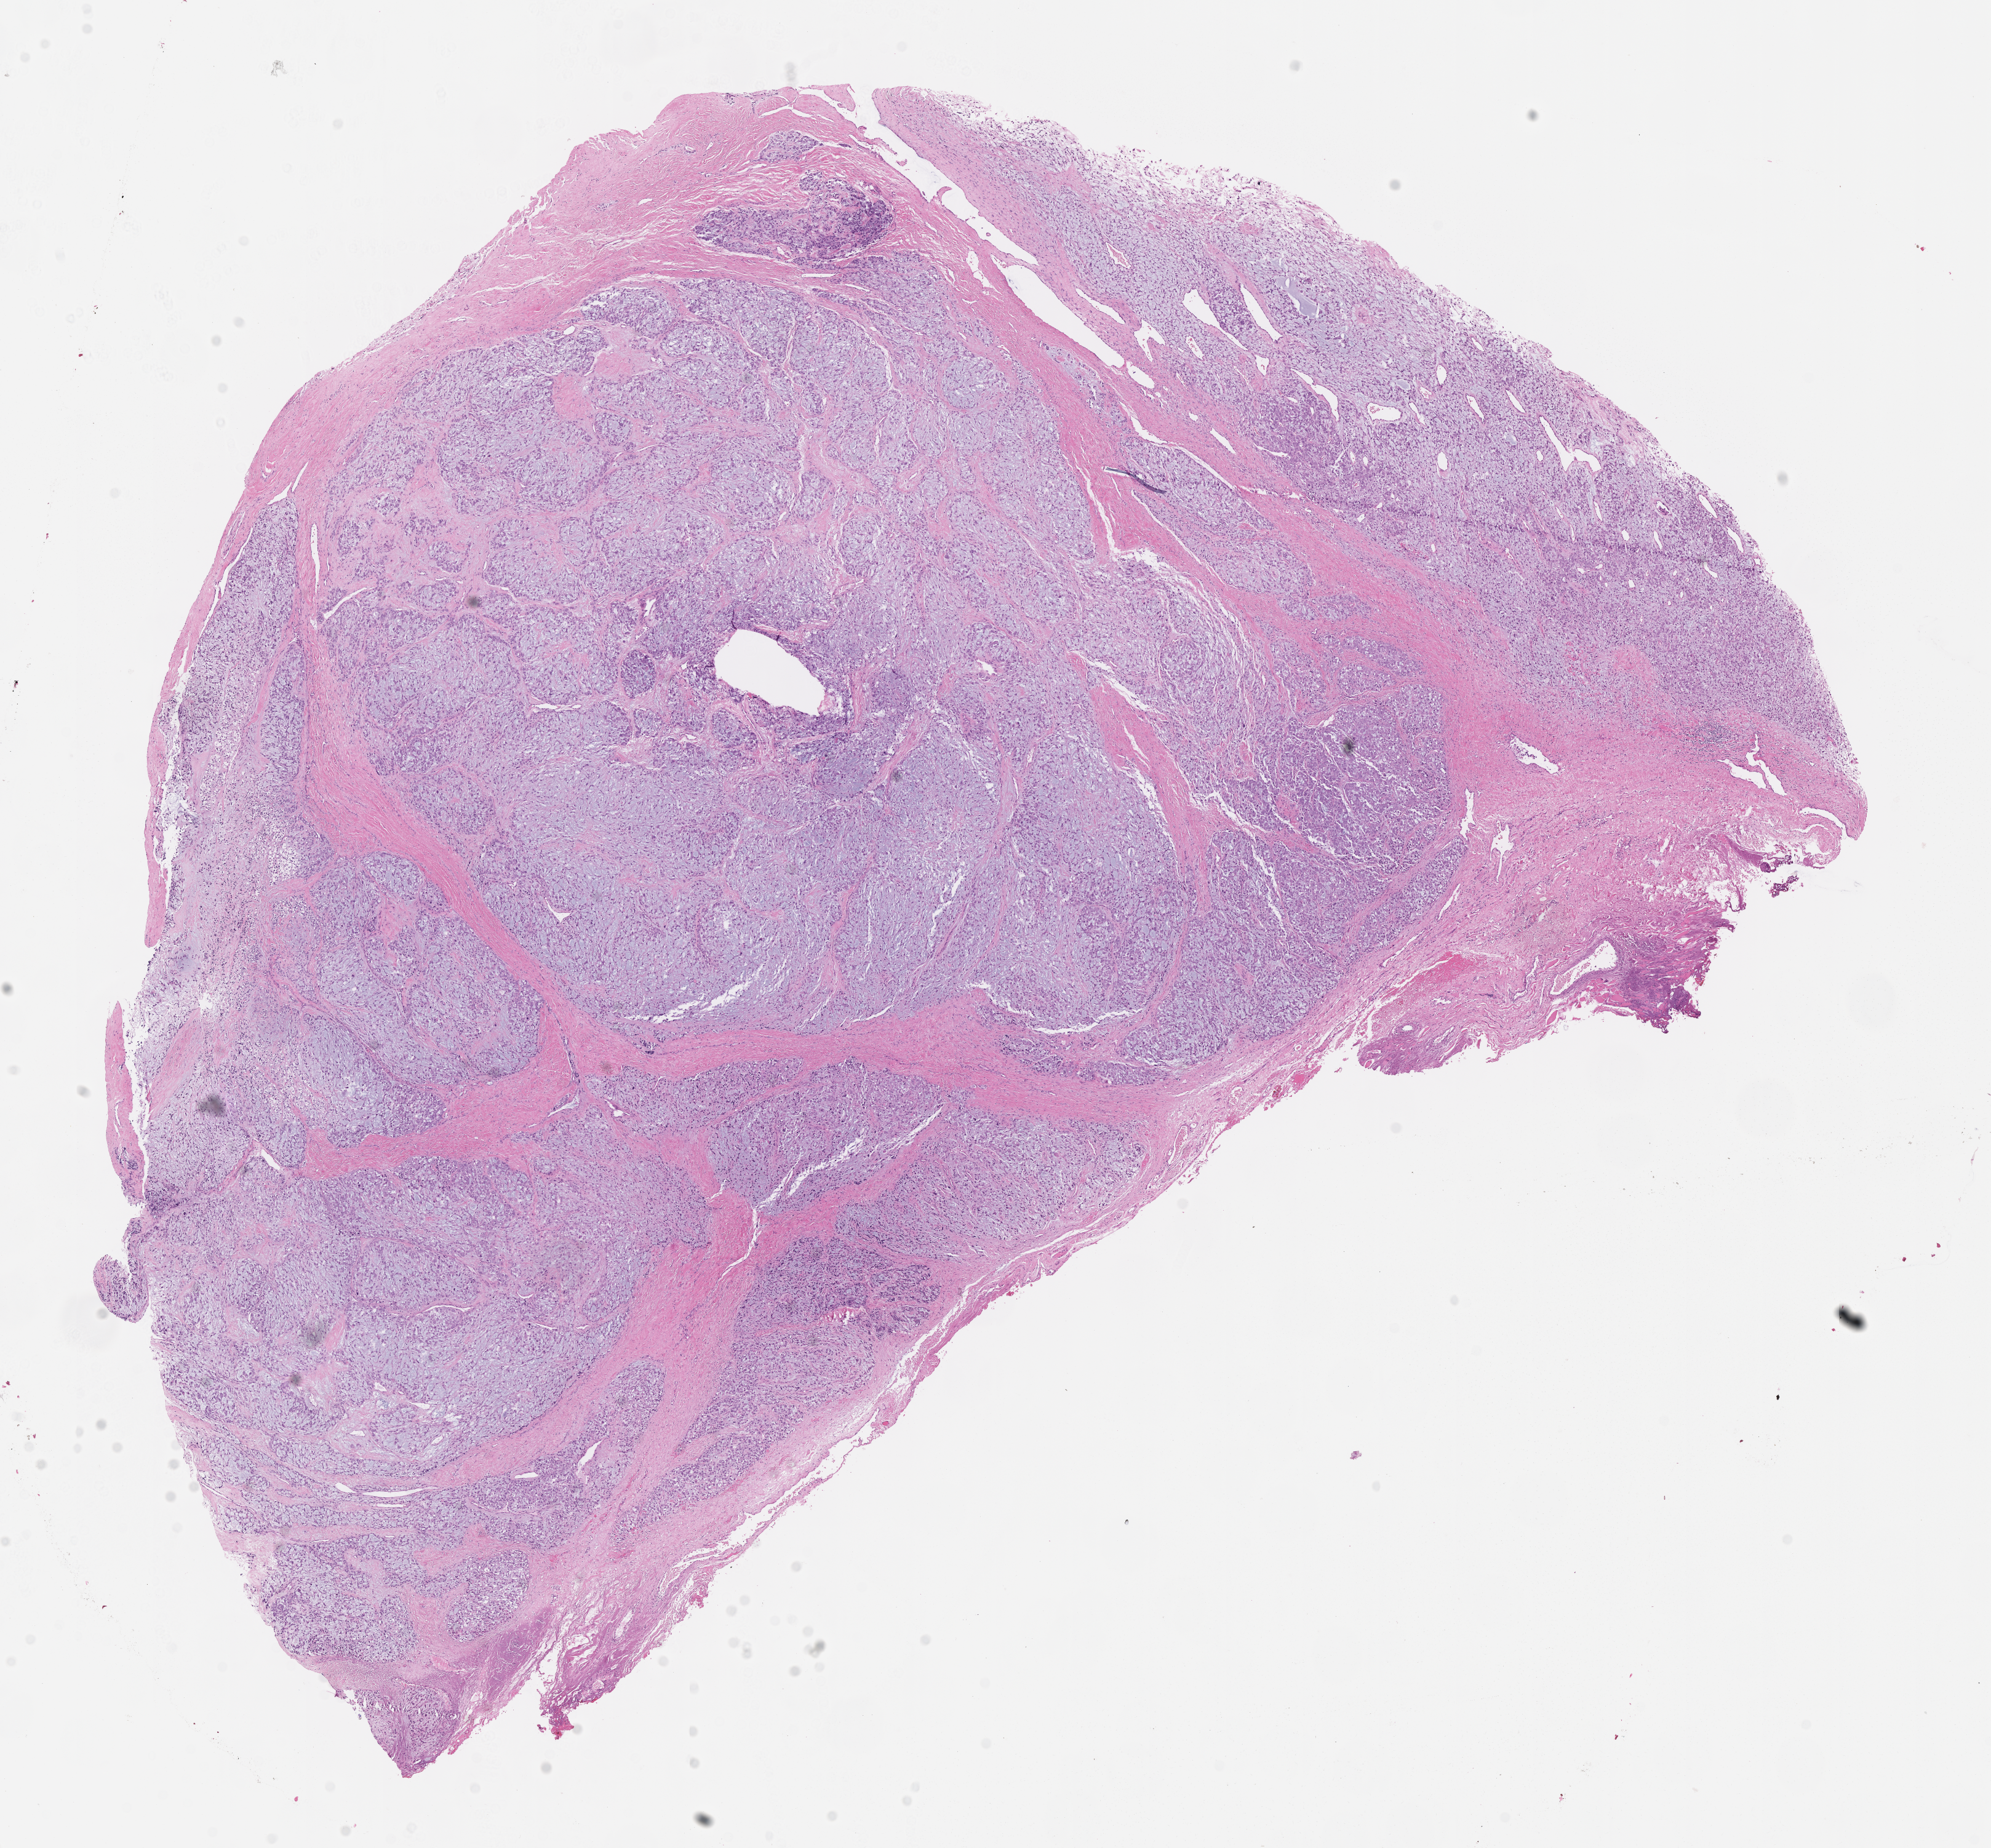
Haematoxylin and eosin whole-slide image of tumor tissue — whole scanned area (about 13.1 x 12.1 mm) shown as a low-resolution overview. Formalin-fixed, paraffin-embedded (FFPE) tissue. Site: soft tissue, spine. Patient: female, age 16.2 years at diagnosis.
Stage (as recorded): 3. Diagnosis: rhabdomyosarcoma; histological classification: embryonal rhabdomyosarcoma. Metastatic status at presentation (as recorded): non-metastatic.